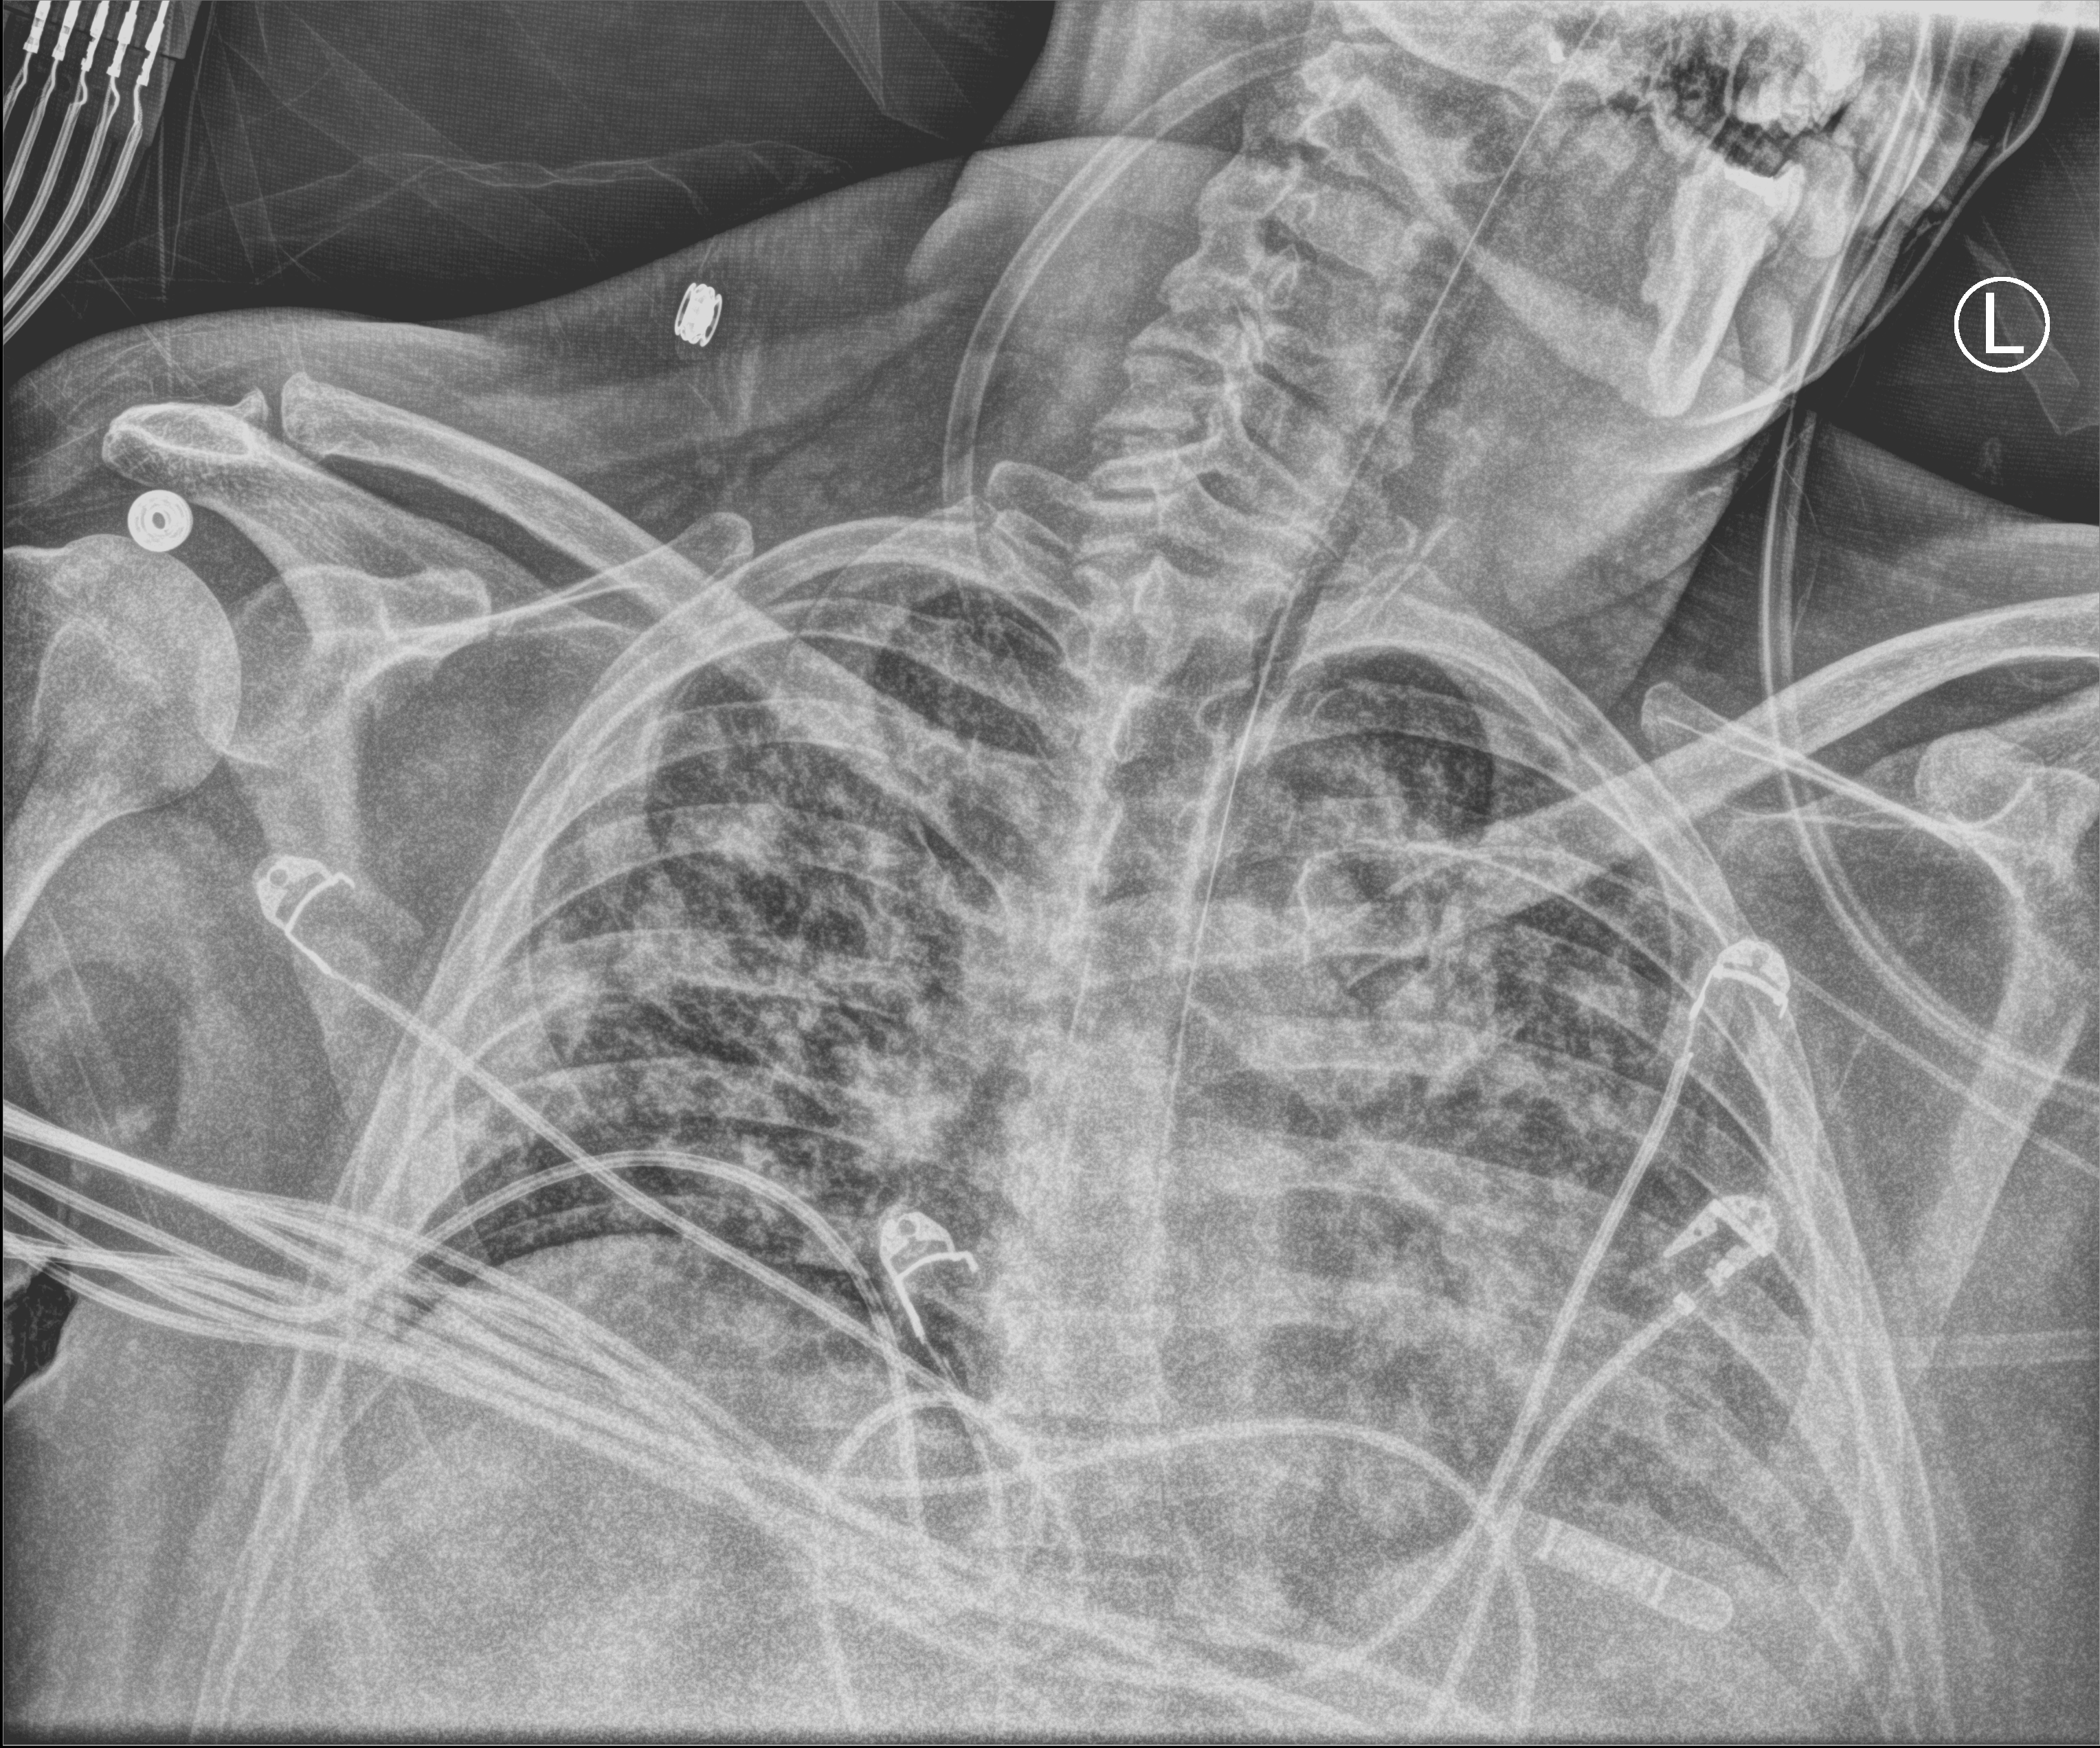
Bedside chest radiograph (computed radiography), anteroposterior (AP) projection. Patient hospitalised with COVID-19; male, aged 18–59 years.
From the hospital-stay record, not from the radiograph (when in the stay this image was taken is not recorded): COPD (admission record): no.